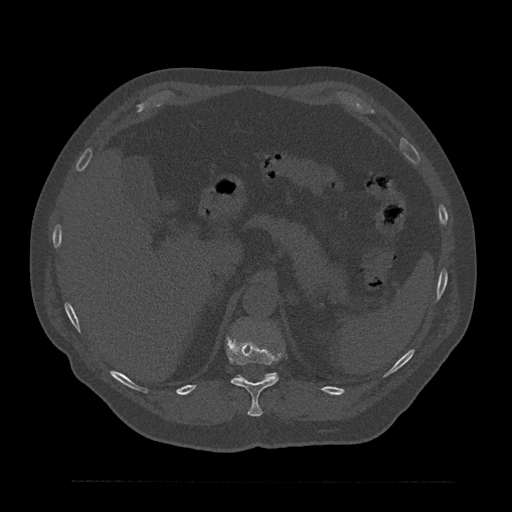
CT including the spine, one axial slice. Position 276 of 797 along the scan axis. 120 kVp. Bone window (W 1800 / L 400 HU). 0.5 mm slice thickness. 512 × 512 image matrix, field of view 430 × 430 mm. Patient: male, 61 years. Case-level facts recorded for this patient, not image findings: primary cancer: prostate.
Outlined on this slice (semi-automatically segmented with operator editing):
- T11 vertebra: bounding box <226,336,282,417> (left, top, right, bottom; pixels)
- T12 vertebra: <267,373,275,377>